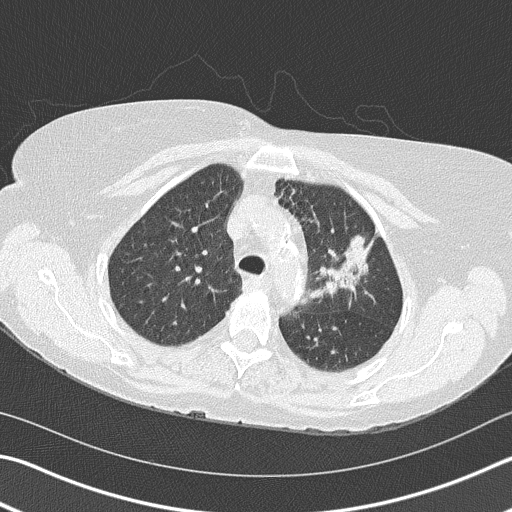
Chest CT (low-dose screening protocol), one axial image. Second annual screen. Lung window (W 1500 / L -600 HU). 2 mm slice thickness. 512 × 512 image matrix. Female, age 68 years at enrolment. Former smoker at enrolment.
- Expert-annotated lung lesion, bounding box (x1, y1, x2, y2) in pixels: (292, 211, 385, 316).
- Reader record for this screening exam (exam-level; its link to the box is not recorded): non-calcified nodule or mass ≥4 mm, left upper lobe, 4 × 2 mm, spiculated (stellate) margins, soft tissue attenuation, pre-existing on the prior screen: yes; interval growth: yes.
- Participant outcome: lung cancer diagnosed 392 days after this screen — adenocarcinoma, NOS, left upper lobe, poorly differentiated (G3), stage IB (AJCC 6th edition), 50 mm at pathology.